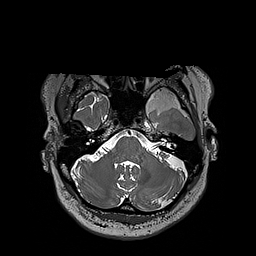
Brain MRI from a brain-tumour surgery series, one axial slice; slice 152 of 192 in the series (ordered by position); 1 mm slice thickness; 256 × 256 image matrix, field of view 250 × 250 mm. From the clinical record (not read from this slice): histopathology: Oligodendroglioma; WHO grade: 3; IDH mutation: yes; tumour location: Left Sylvian Fissure (Temporal).
Structures marked on this image (expert manual segmentation):
- tumour: bounding box [x1, y1, x2, y2] px = [124, 89, 197, 112]